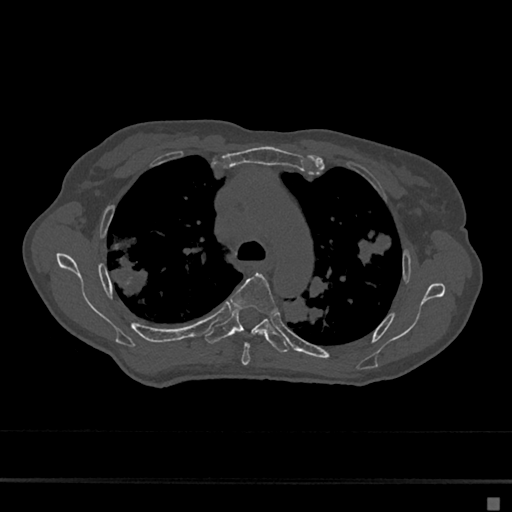
CT including the spine, one axial slice; slice 482 of 797 in the series (ordered by position); bone window (W 1800 / L 400 HU); 512 × 512 image matrix, field of view 360 × 360 mm. Patient: female, 68 years. Case-level facts recorded for this patient, not image findings: primary cancer: renal.
Outlined on this slice (semi-automatically segmented with operator editing):
- T4 vertebra: bounding box <230,273,278,366> (left, top, right, bottom; pixels)
- T5 vertebra: <205,309,289,353>